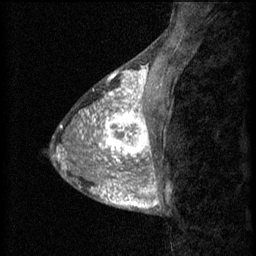
Breast MRI (dynamic contrast-enhanced), one sagittal slice; slice 20 of 60 in the series (ordered by position); 3 images stored at this slice position (order not interpretable as contrast timing); 1.5 T; TE 4.2 ms, TR 8.2 ms; 256 × 256 image matrix, field of view 180 × 180 mm. Female patient, age 38 years.
Outlined on this slice (semi-automatically segmented with operator editing):
- analysis volume of interest (the breast-tissue region the enhancement analysis was run in; not a lesion): bounding box <95,106,157,171> (left, top, right, bottom; pixels)
- tumour enhancement mask (voxels above the 70 % enhancement threshold inside the analysis volume of interest): <95,106,154,171>